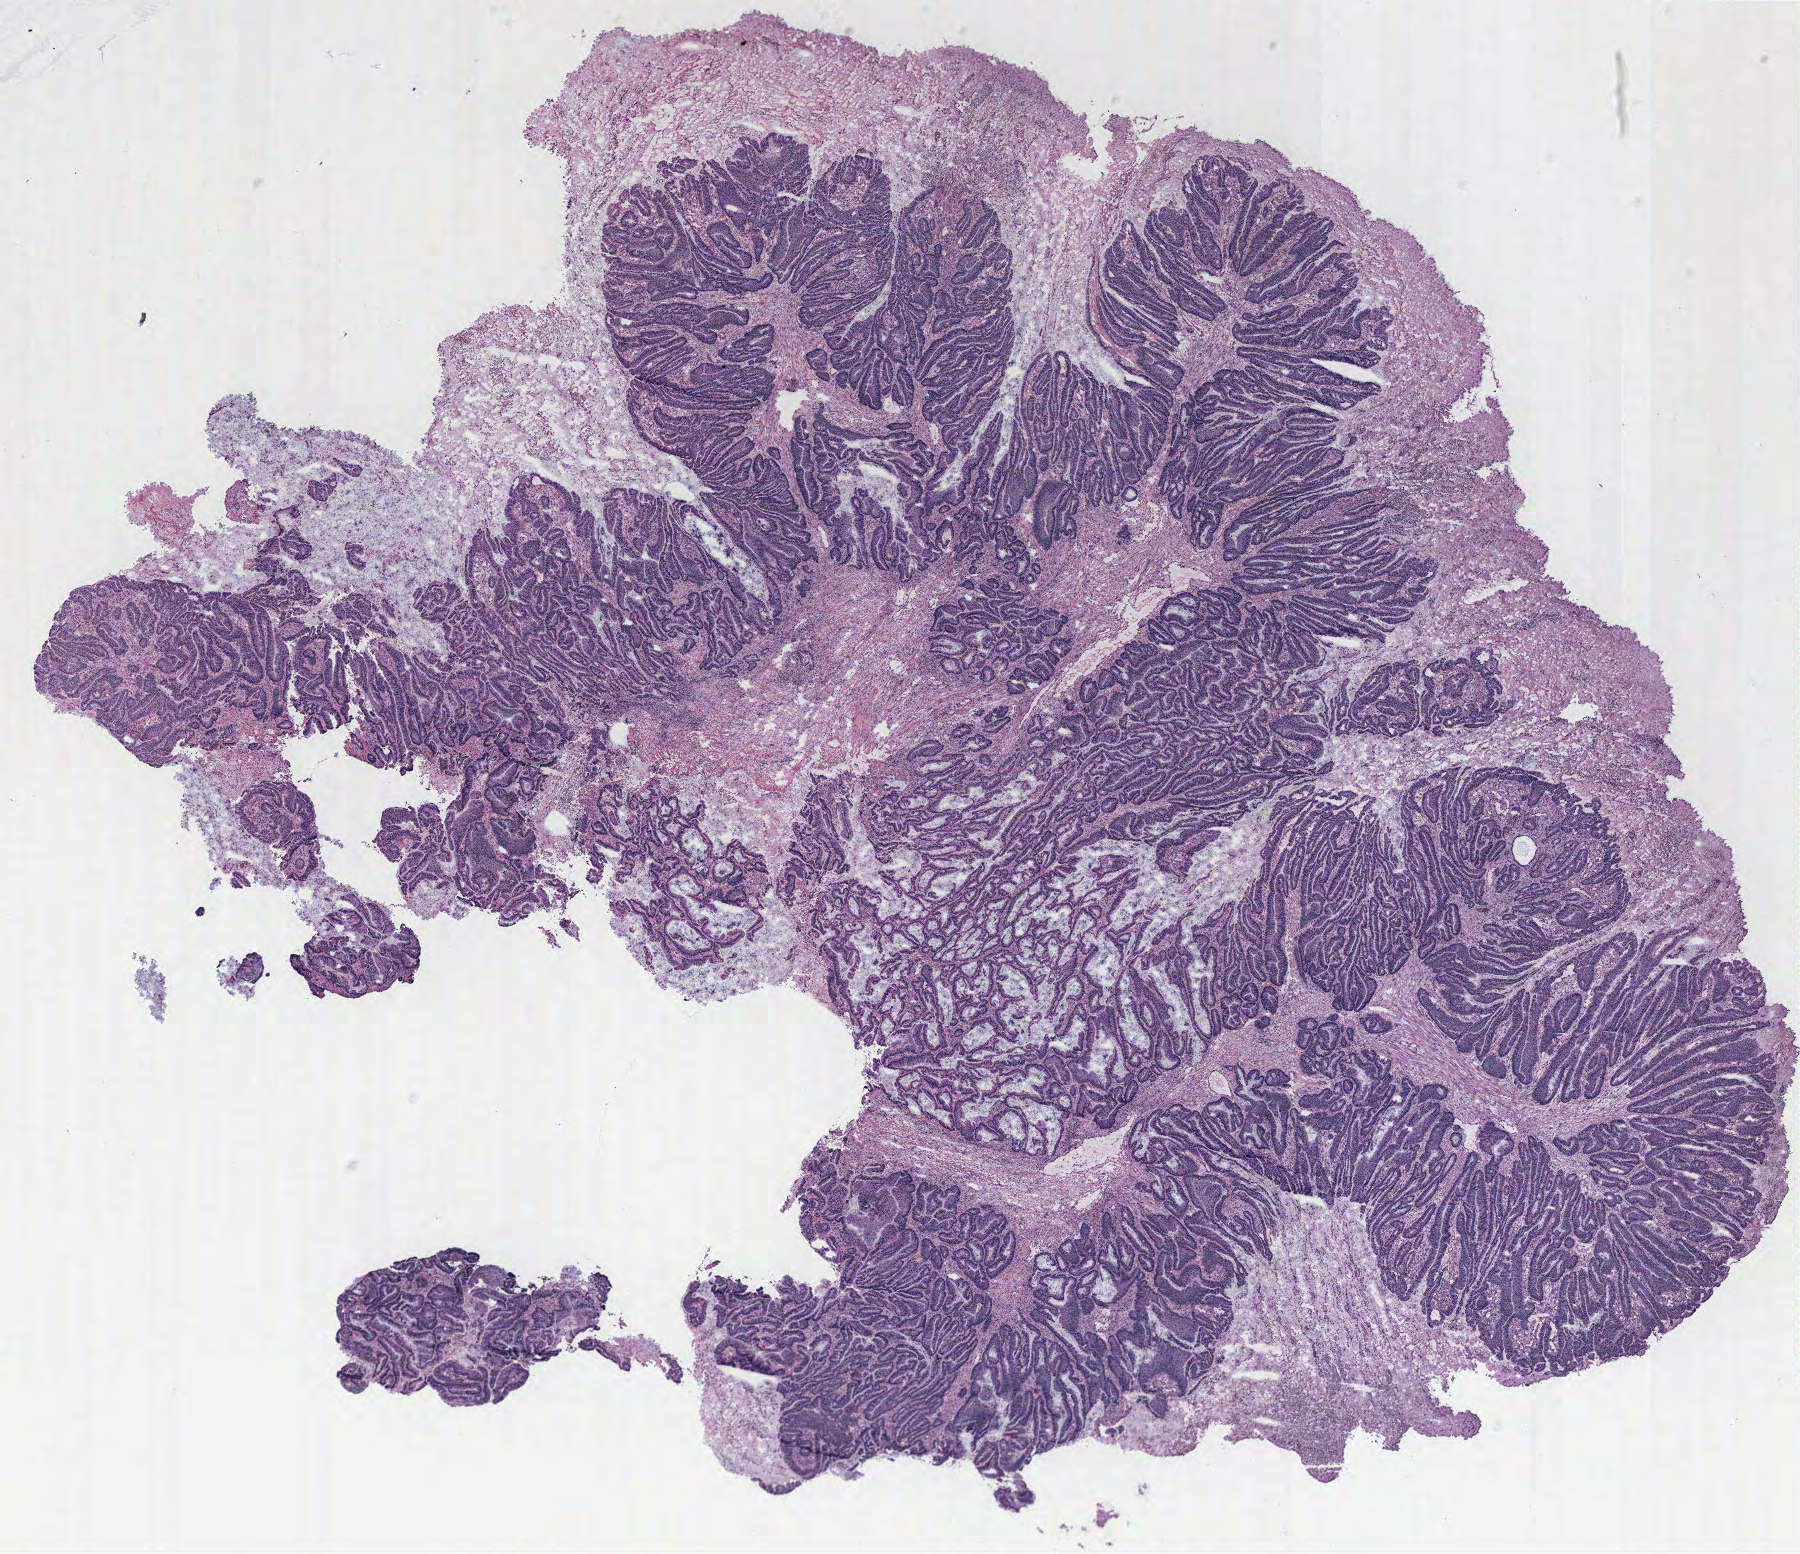
Digitized H&E tissue section (whole slide) — low-resolution overview of the scanned area, about 14.4 x 12.4 mm (slide scanned at 40x); colon, normal (non-tumour) tissue. 76-year-old female patient.
This section: normal (non-tumour) tissue from the same patient. Patient diagnosis: Adenocarcinoma, NOS.